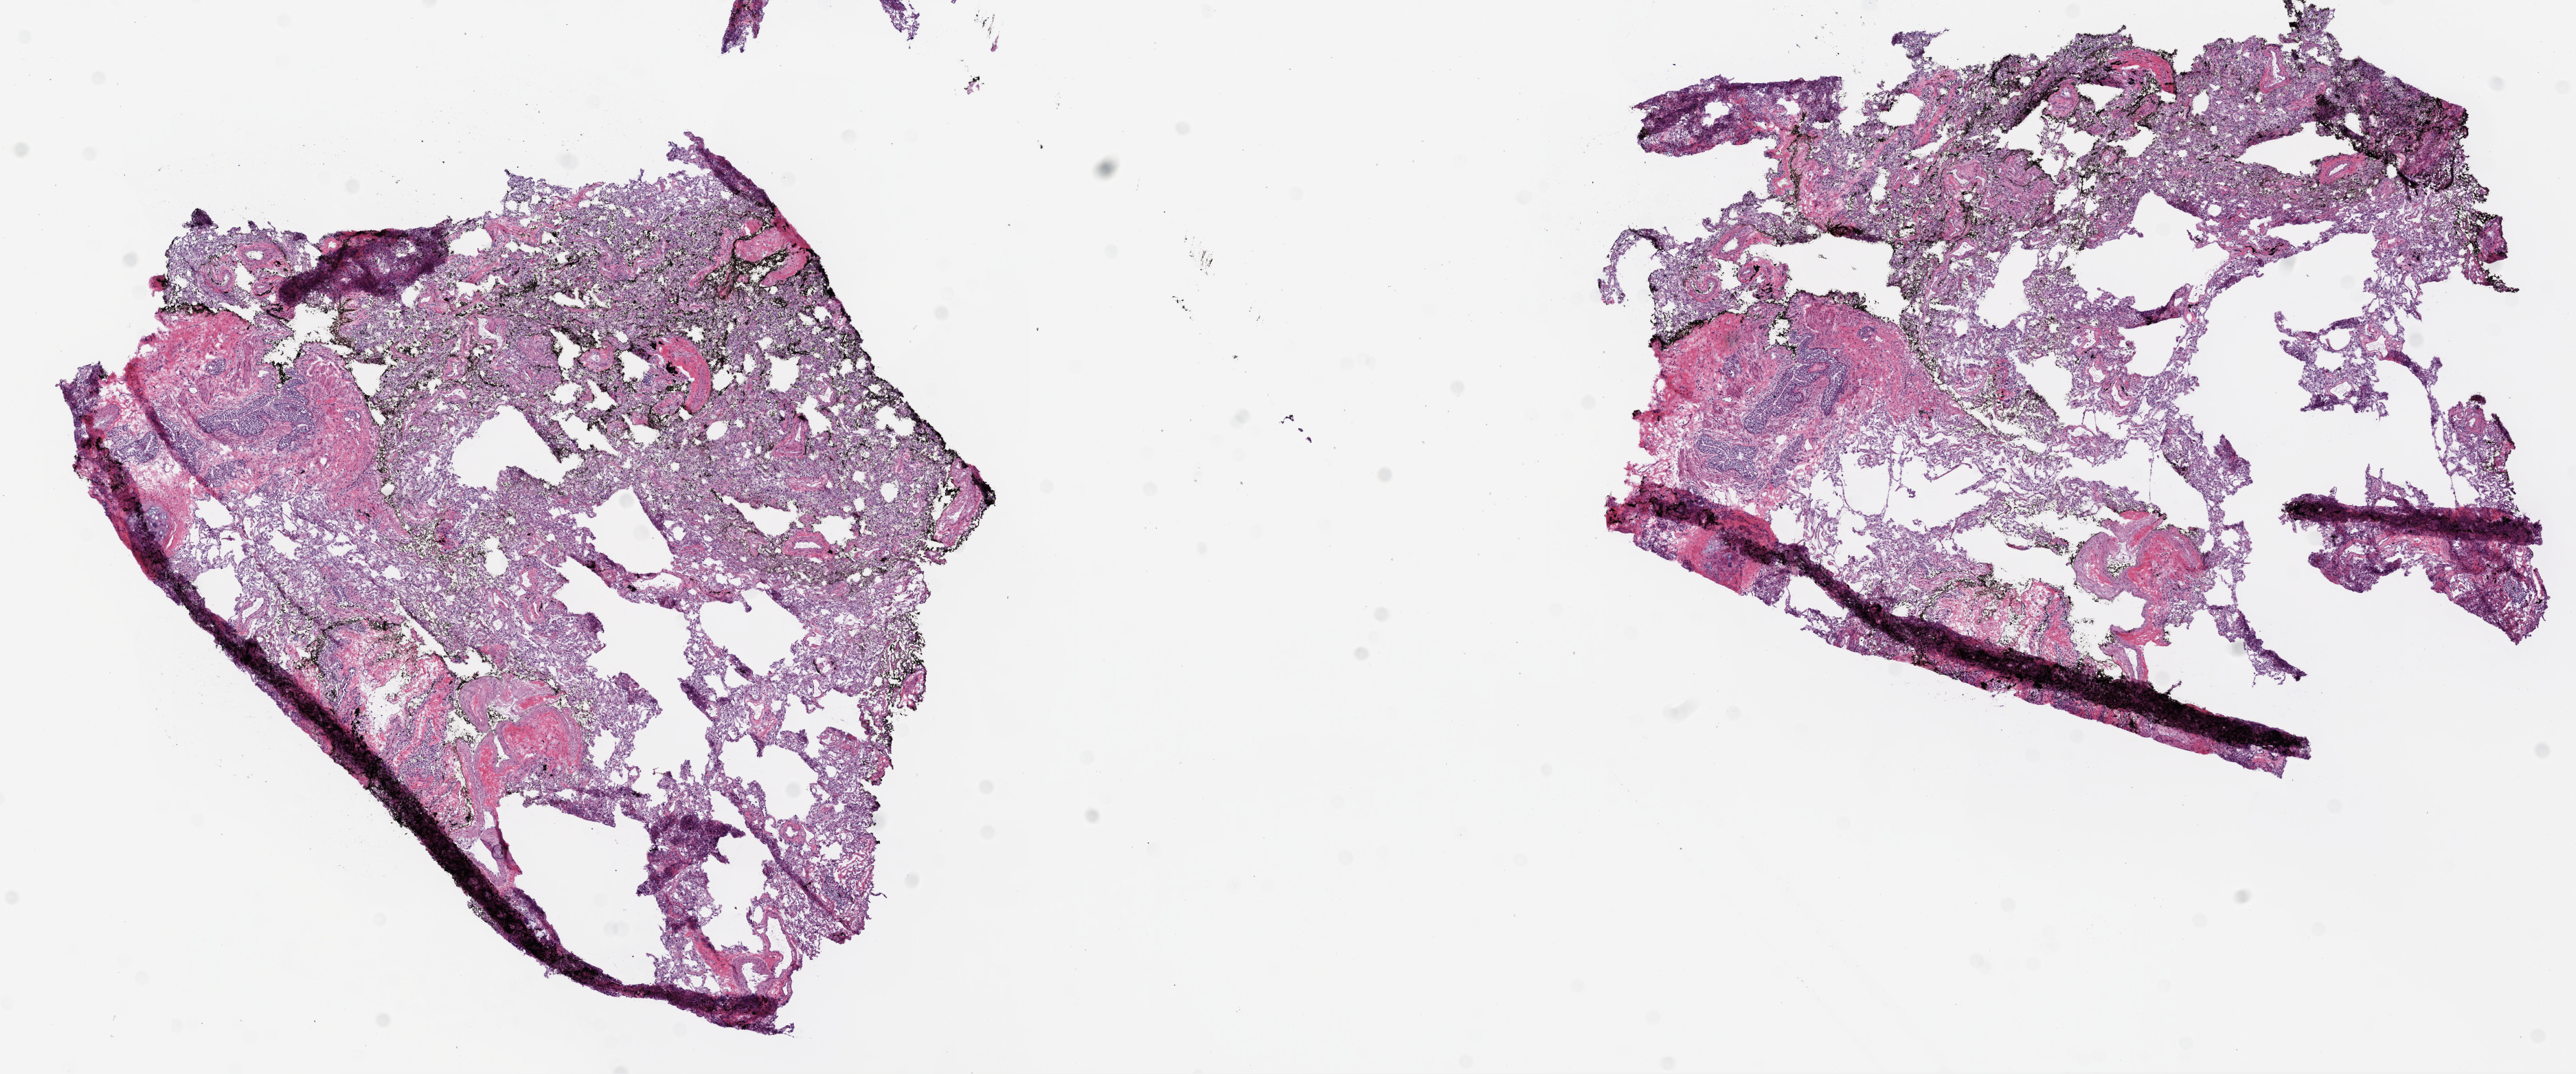
Digitized H&E tissue section (whole slide), shown as a low-resolution overview of the whole scanned area (about 15.0 x 6.3 mm, from a 20x scan). Frozen section from the top of the tissue portion. Lung, solid tissue normal (non-tumour tissue) sample. Female, age 74 years at initial diagnosis.
This section: solid tissue normal sample (biorepository sample class). Patient diagnosis: Clear cell adenocarcinoma, NOS (lower lobe, lung).